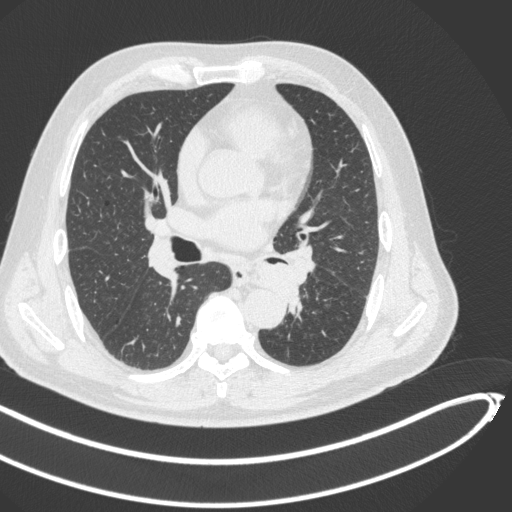
Chest CT, one axial slice. Position 249 of 466 along the scan axis. 120 kVp. Lung window (W 1500 / L -600 HU). 1 mm slice thickness. 512 × 512 image matrix. Patient: male, 64 years. From the clinical record (not read from this slice): clinical TNM (as recorded): T1c N0 M0; histopathological grade: G2.
Structures marked on this image (bounding box drawn by a radiologist):
- lung tumour (recorded histology: squamous cell carcinoma): bounding box [x1, y1, x2, y2] px = [250, 258, 308, 314]